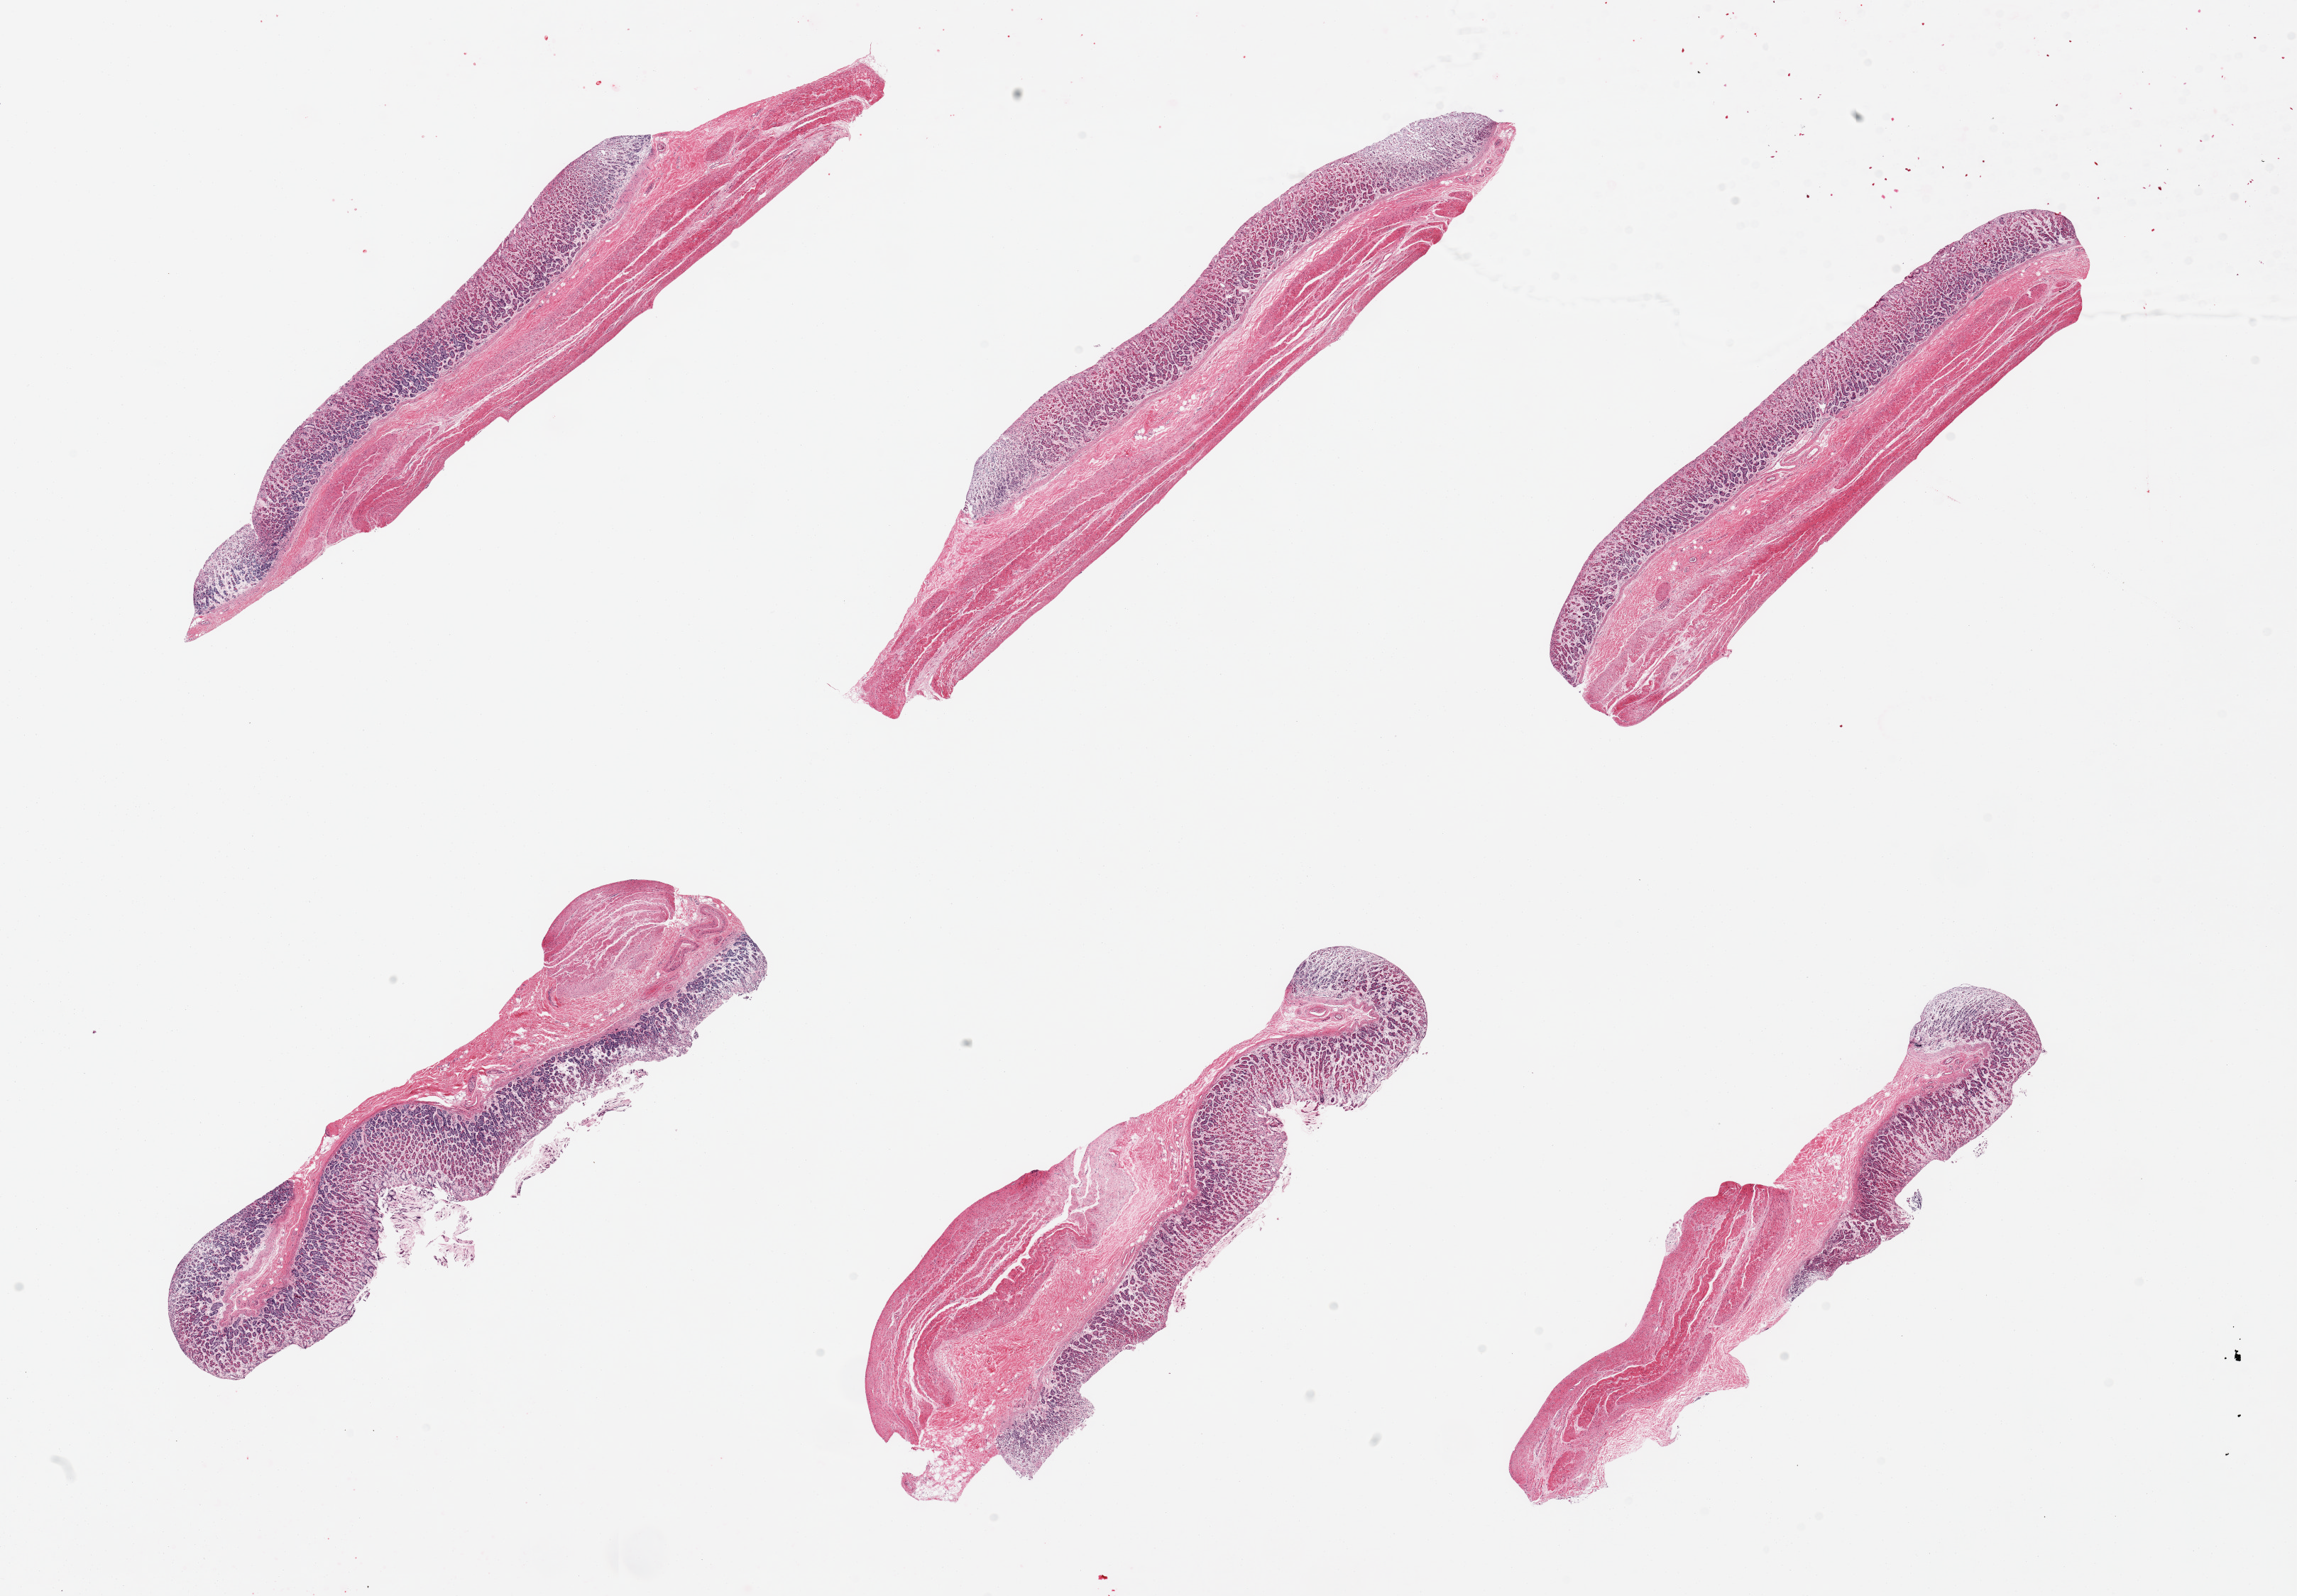
Digitized hematoxylin and eosin (H&E)-stained section, a low-resolution overview of the entire scanned area, about 25.6 x 17.8 mm, PAXgene-fixed paraffin-embedded (PFPE) section, sampled site (target tissue): stomach, donor tissue sample. Male donor.
Reviewer comment on this tissue sample: 6 pieces, mucosa up to ~0.8mm, variably preserved but generally moderate-markedly advanced autolysis.